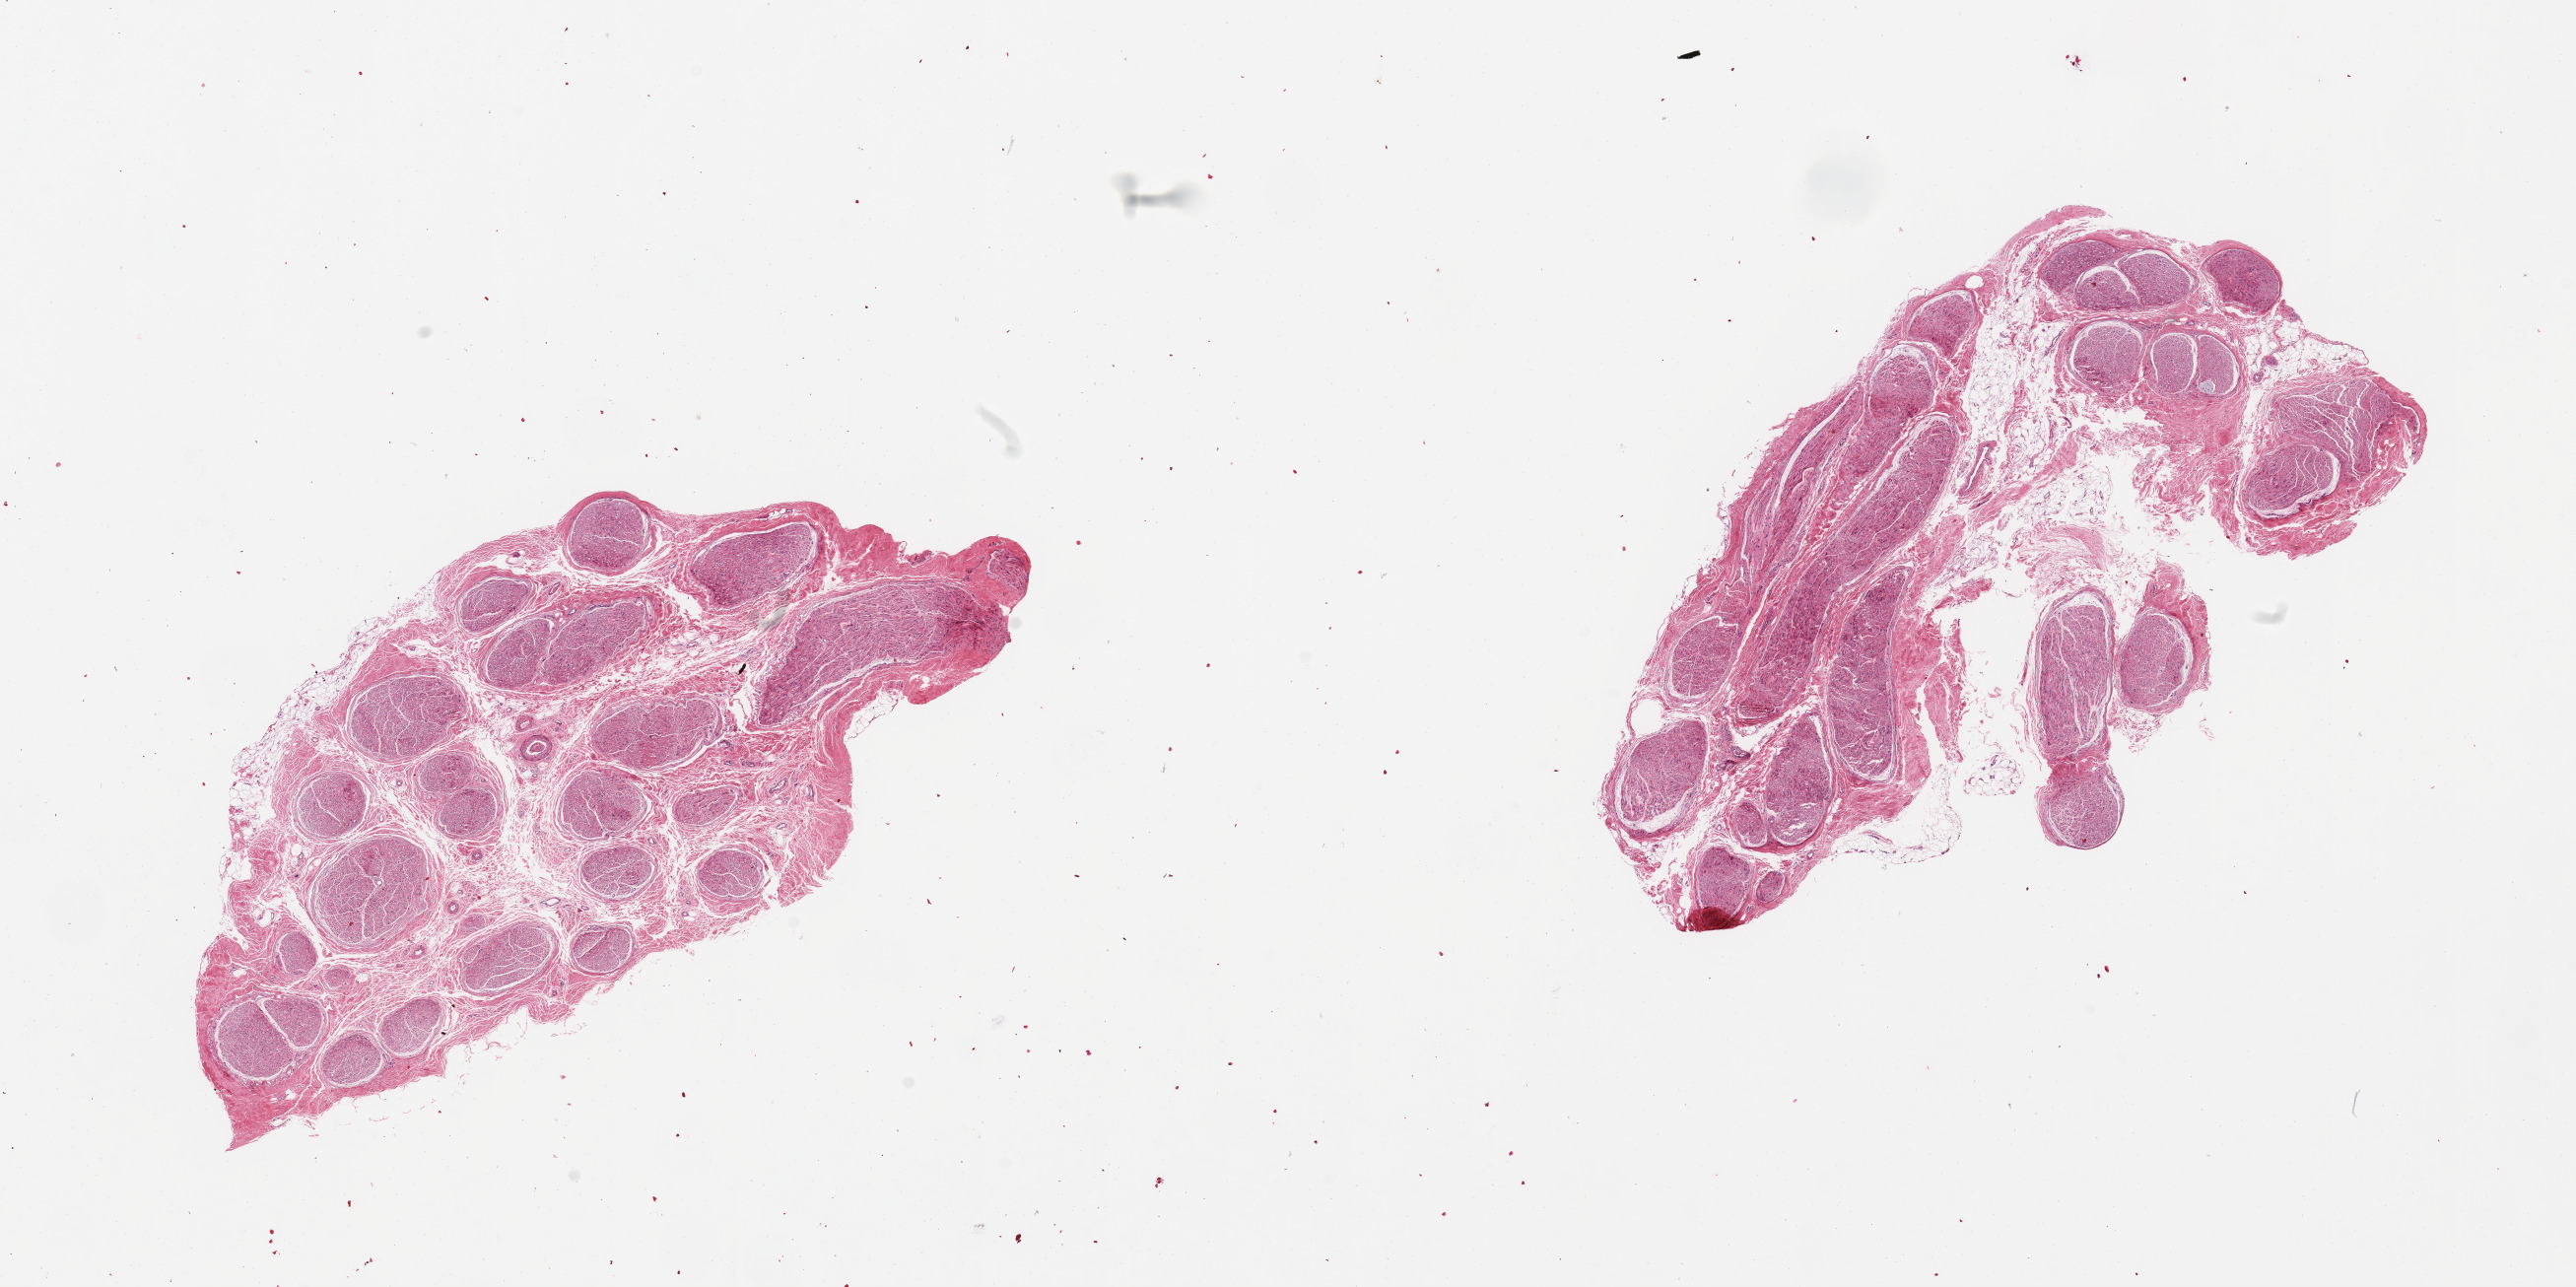
Digitized haematoxylin and eosin-stained section, brightfield, low-resolution overview of the scanned area, about 20.7 x 10.3 mm, PAXgene-fixed, paraffin-embedded tissue, section of tibial nerve (target tissue), tissue donor sample. Donor: male.
Reviewer comment on this tissue sample: 2 pieces; 1 with trivial attachment of fat, 2nd has at least 20% mostly internal fat (incomplete section).